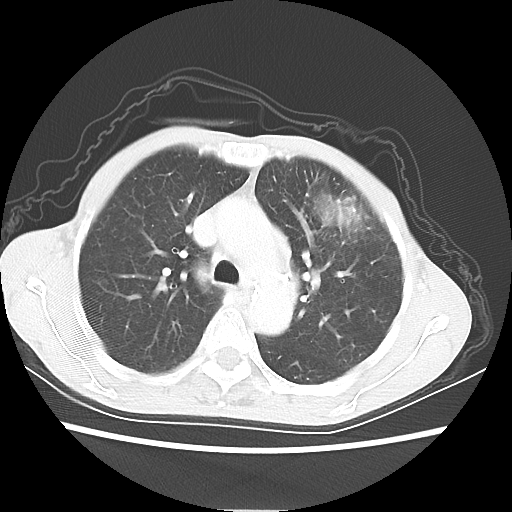
Chest CT, one axial slice. Position 41 of 56 along the scan axis. Reconstruction kernel LUNG. 80 kVp. Lung window (W 1500 / L -600 HU). 512 × 512 image matrix, field of view 331 × 331 mm. Female patient, age 60 years. Case-level facts recorded for this patient, not image findings: clinical TNM (as recorded): T4 N1 M0.
Structures marked on this image (rectangle marked by the reading radiologist):
- lung tumour (recorded histology: adenocarcinoma): bounding box <312,183,366,240> (left, top, right, bottom; pixels)